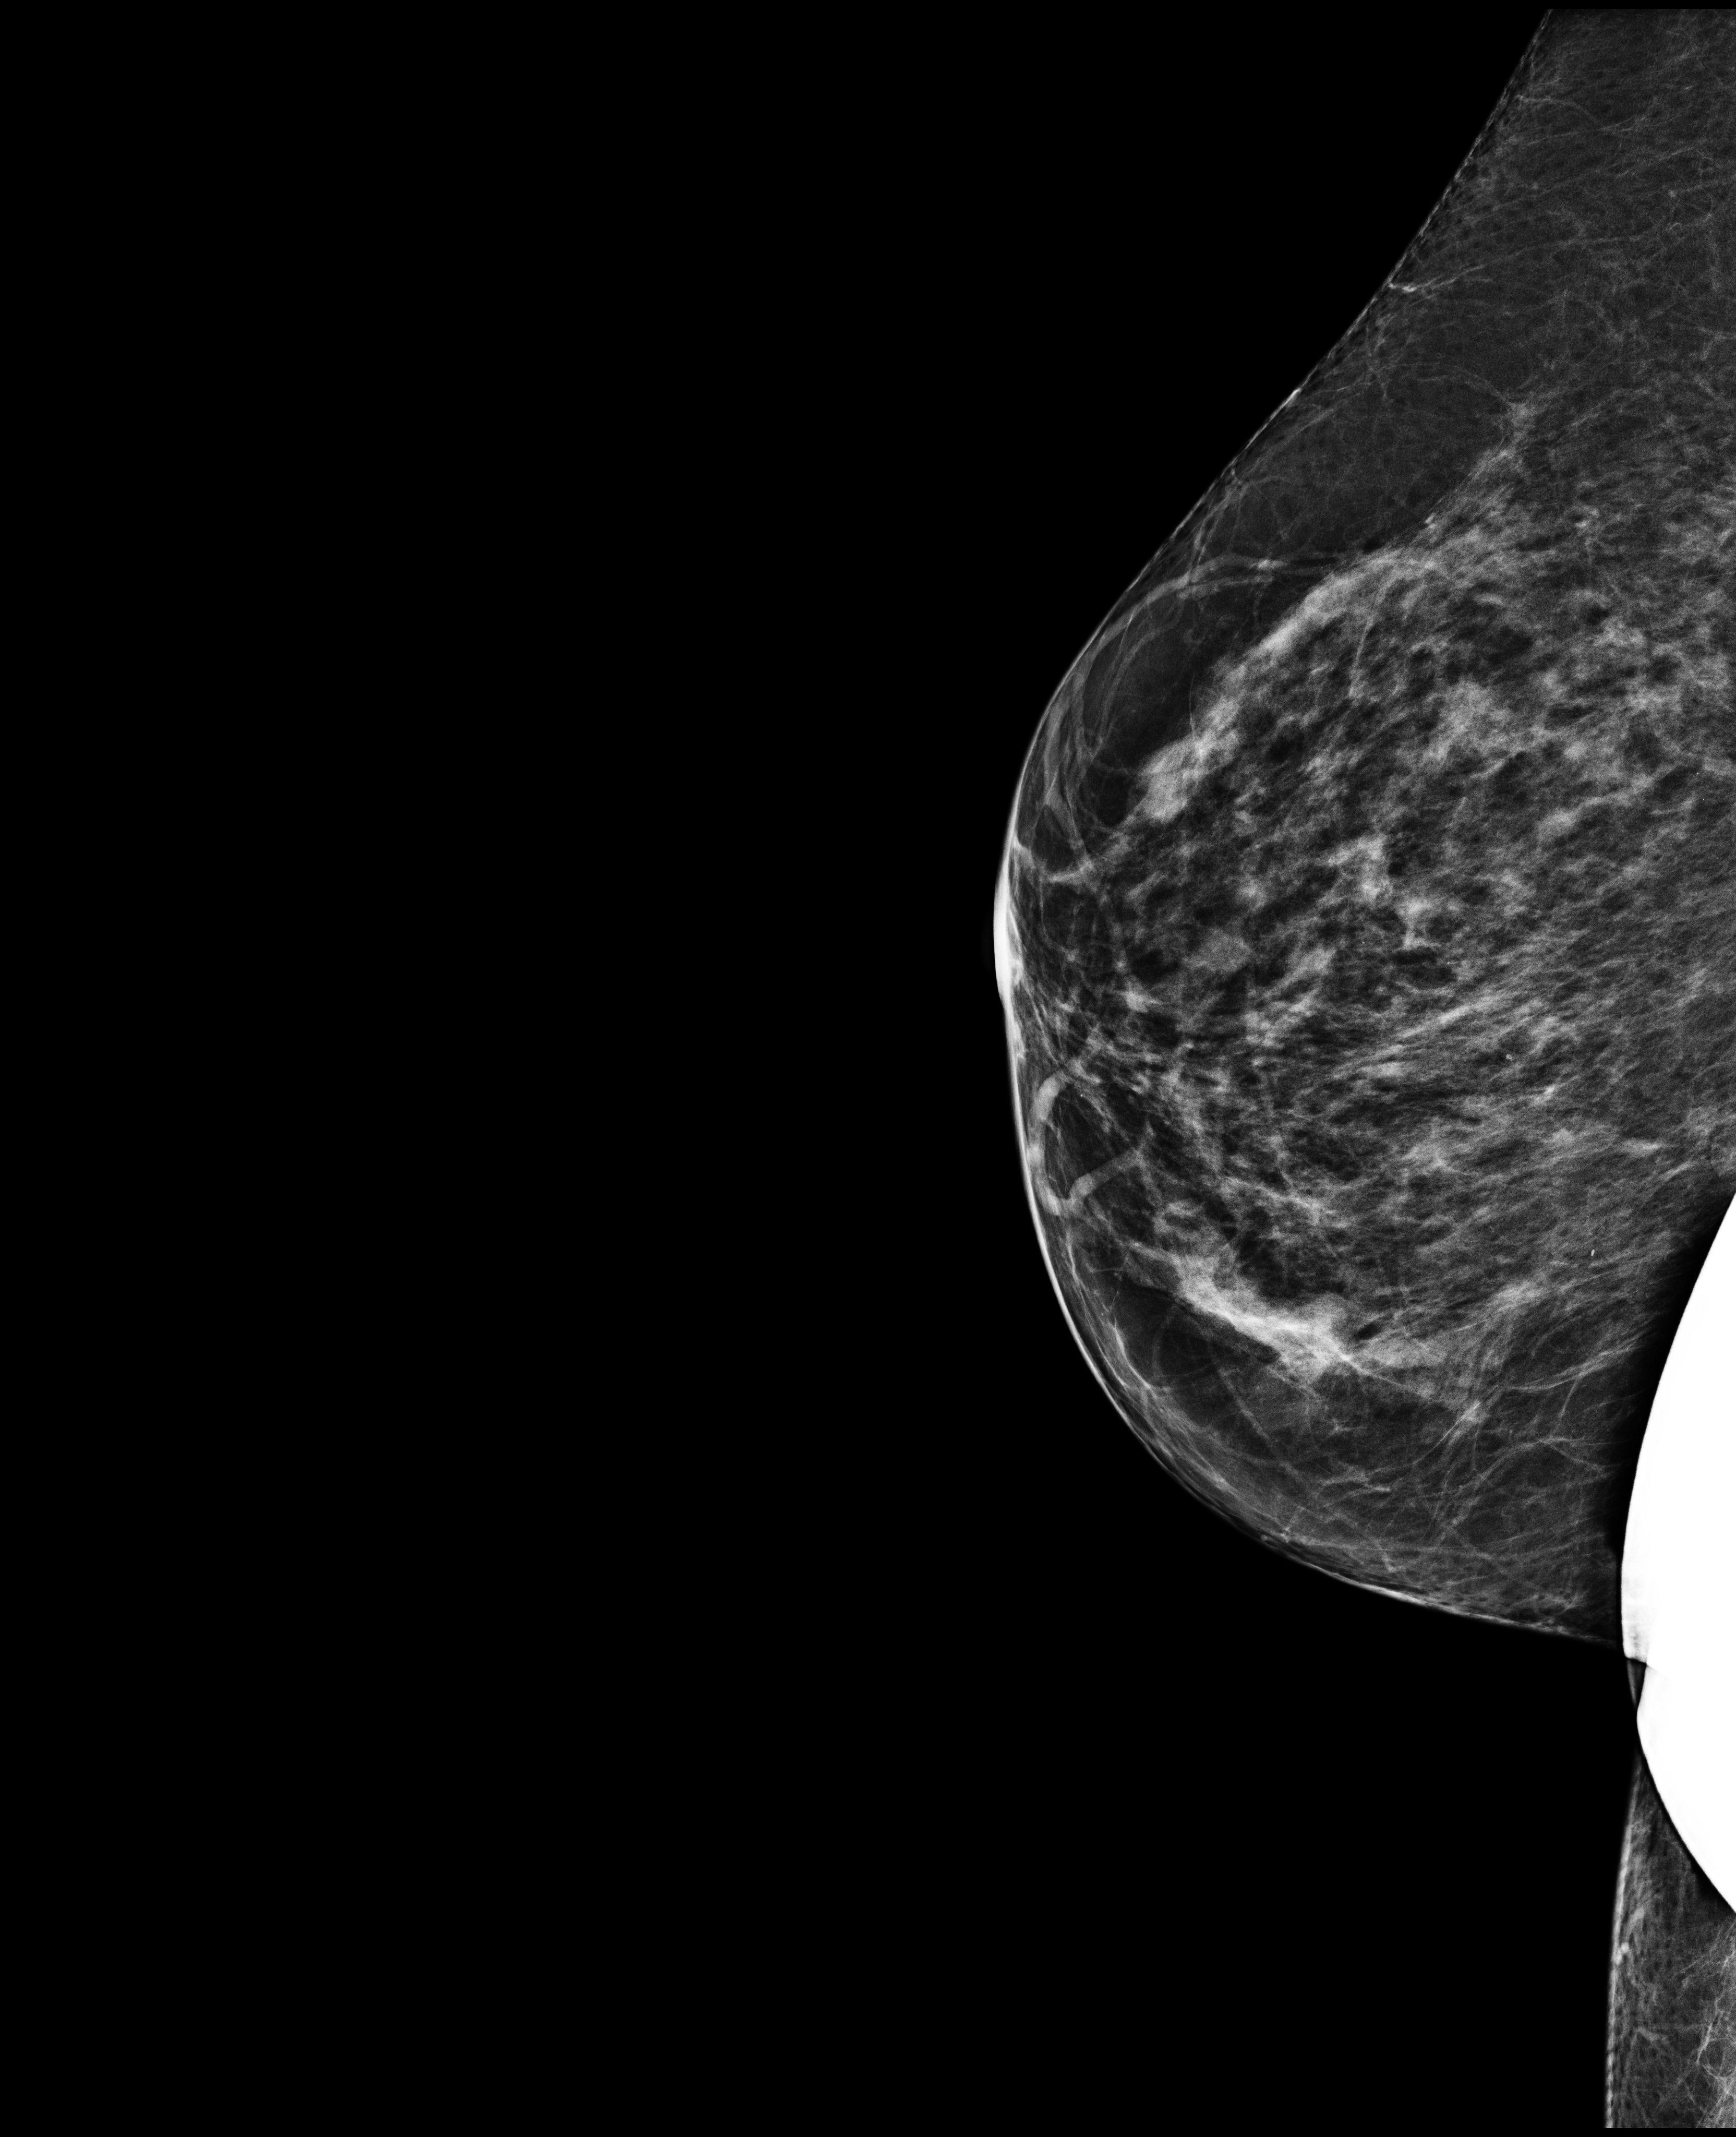
Screening examination. Female patient, age 69 years.
Image type: full-field digital mammogram. Breast: right. Projection: ML view.